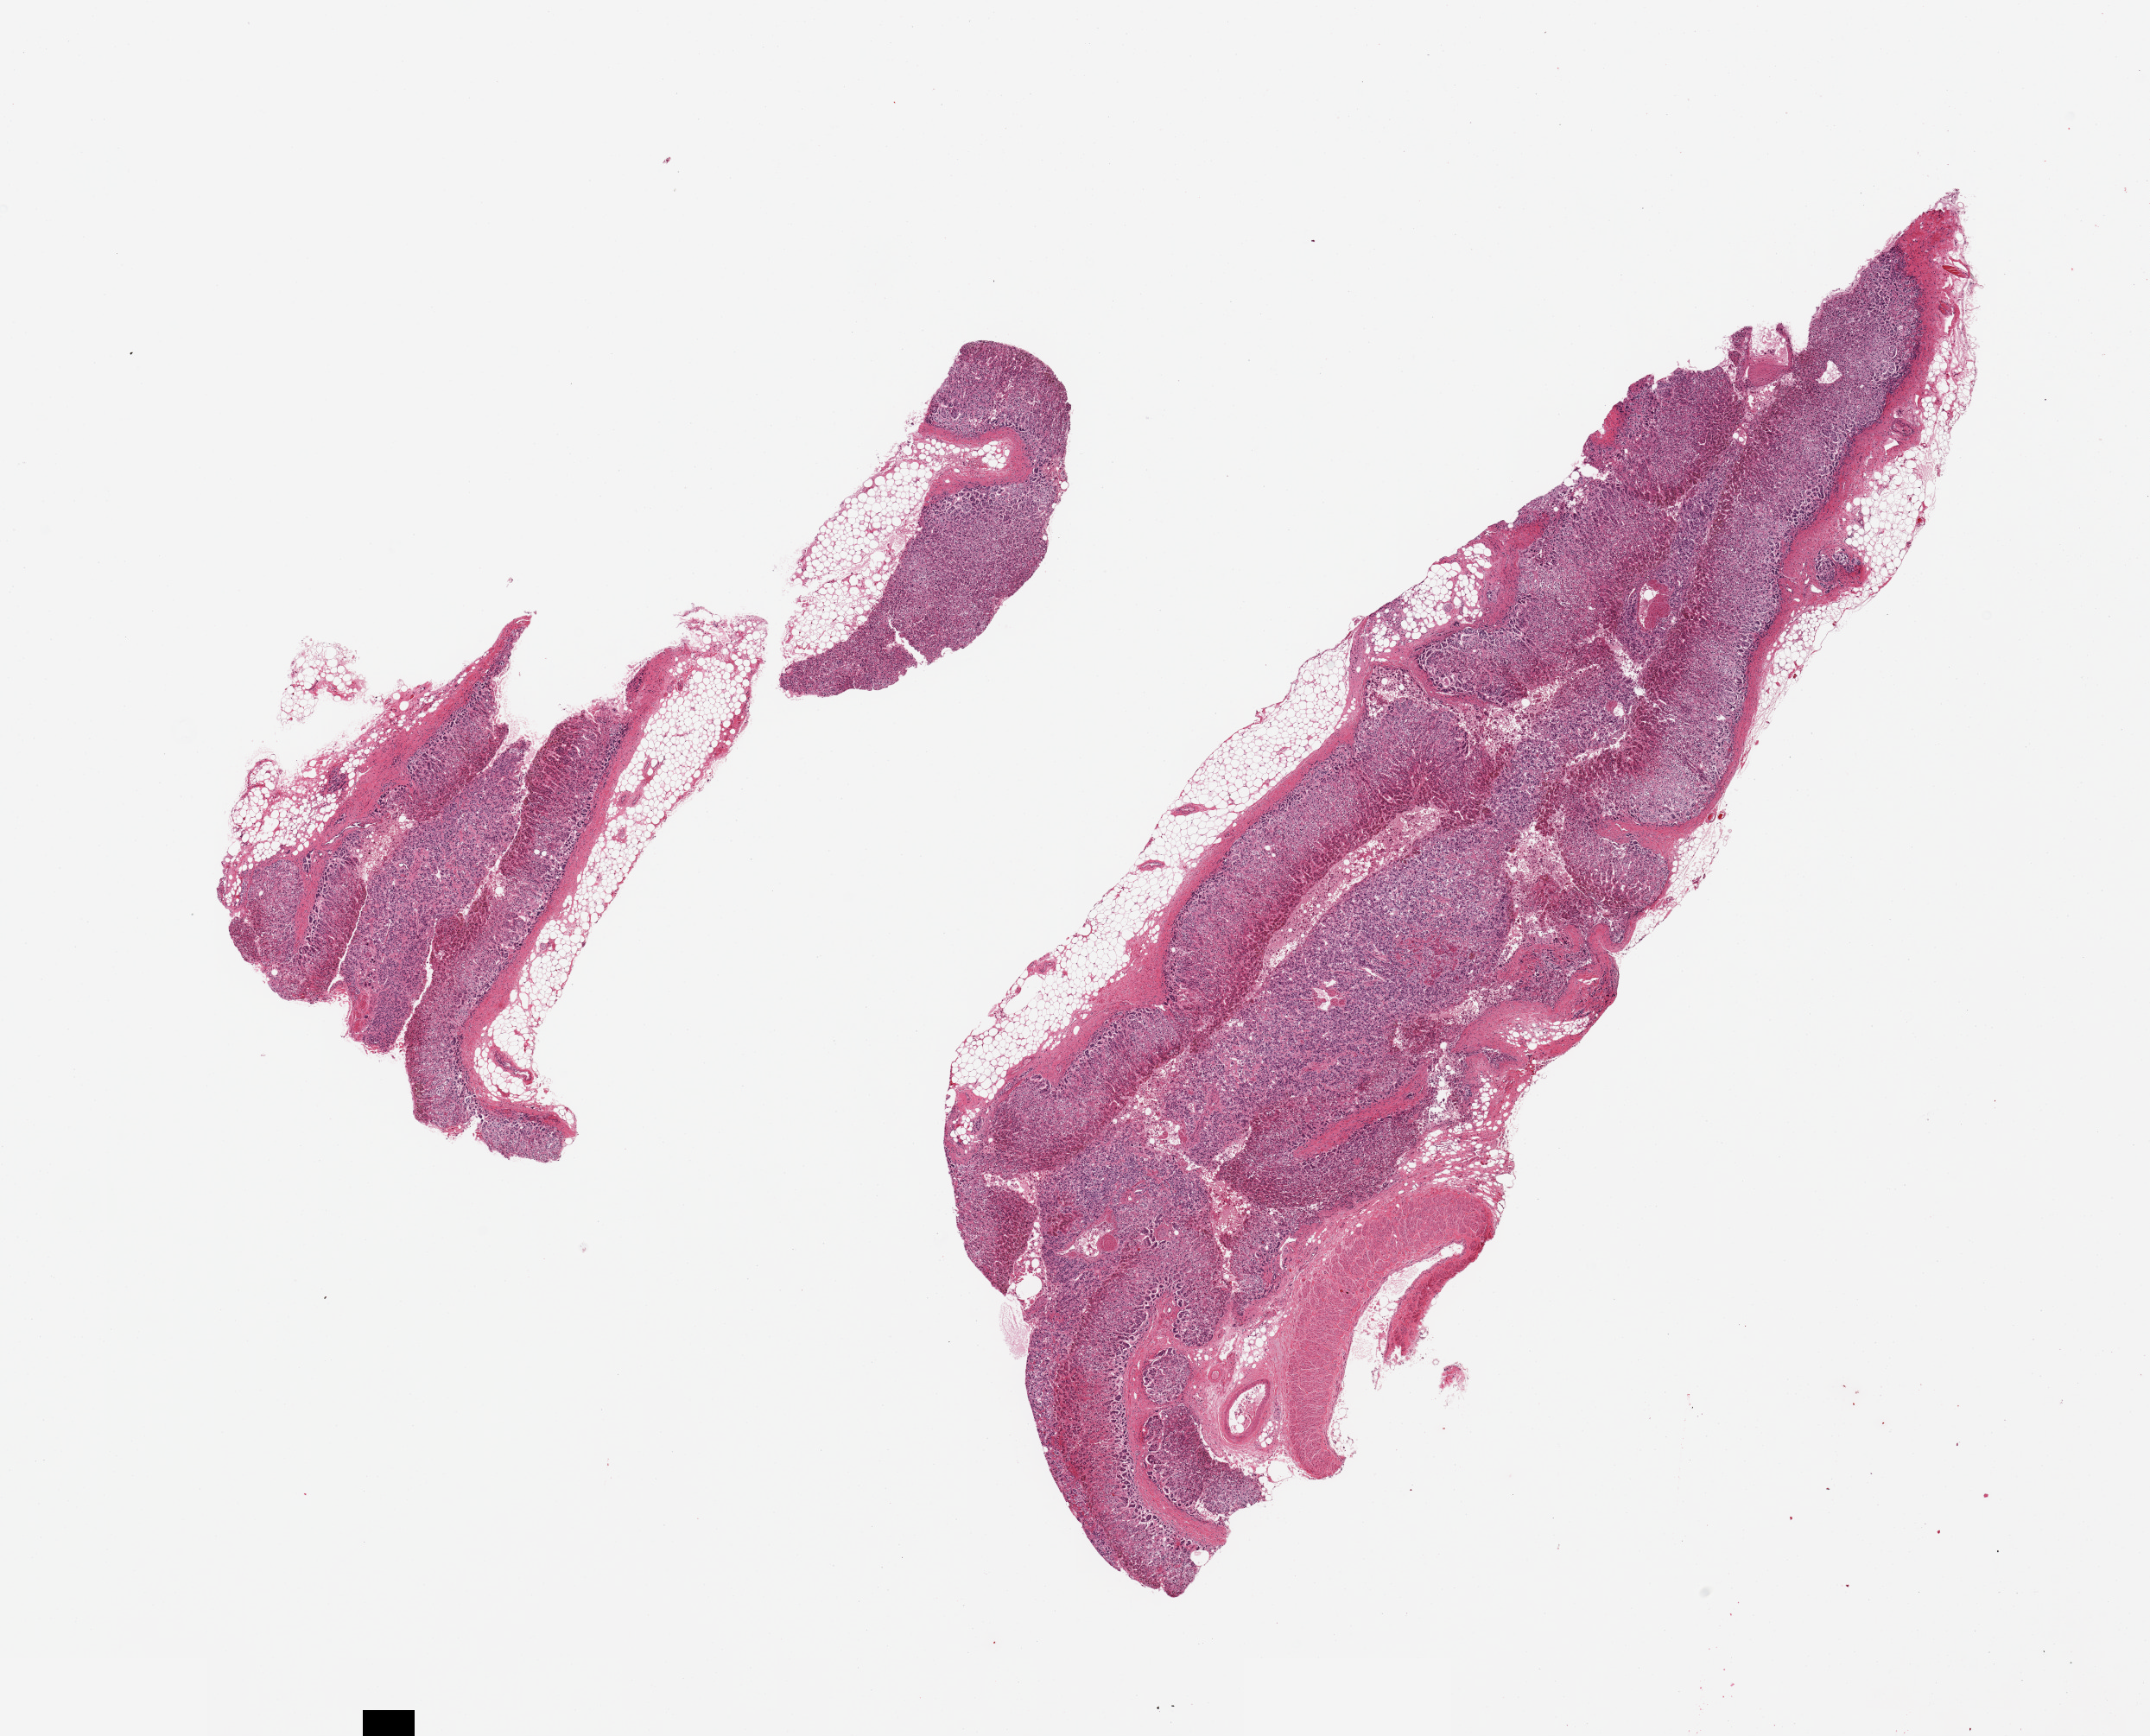
Digitized hematoxylin and eosin (H&E)-stained section — whole scanned area (about 19.7 x 15.9 mm) shown as a low-resolution overview, PAXgene-fixed paraffin-embedded (PFPE) section, target tissue: adrenal gland, donor tissue sample. Donor: female.
Review note (as recorded): 2 pieces; 10% external fat.